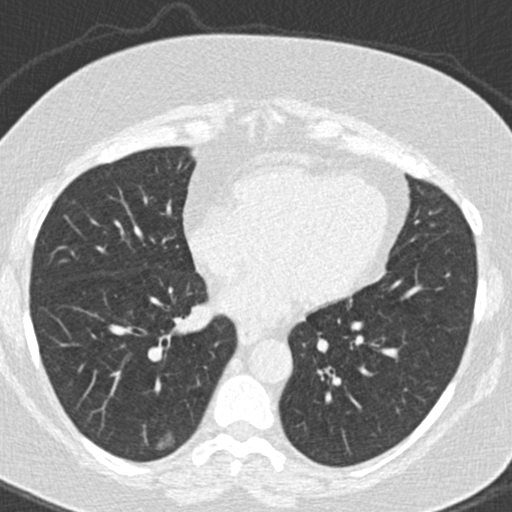
Low-dose screening chest CT, axial slice; baseline screening round; lung window (W 1500 / L -600 HU); 2 mm slice thickness; standard (soft-tissue) reconstruction kernel (B30f). Female, age 63 years at enrolment.
Expert reader's lesion annotation, bounding box (x1, y1, x2, y2) in pixels: (148, 421, 186, 460). Screening reader's record for this exam (one nodule recorded; not confirmed to be the boxed lesion): non-calcified nodule or mass ≥4 mm, right lower lobe, 16 × 10 mm, poorly defined margins, ground glass attenuation. Official screen result: positive, change unspecified: nodule(s) >= 4 mm or enlarging nodule(s), mass(es), or other non-specific abnormalities suspicious for lung cancer. Participant outcome: lung cancer diagnosed 246 days after this screen — bronchiolo-alveolar adenocarcinoma, NOS, right lower lobe, well differentiated (G1), stage IA (AJCC 6th edition), 12 mm at pathology.